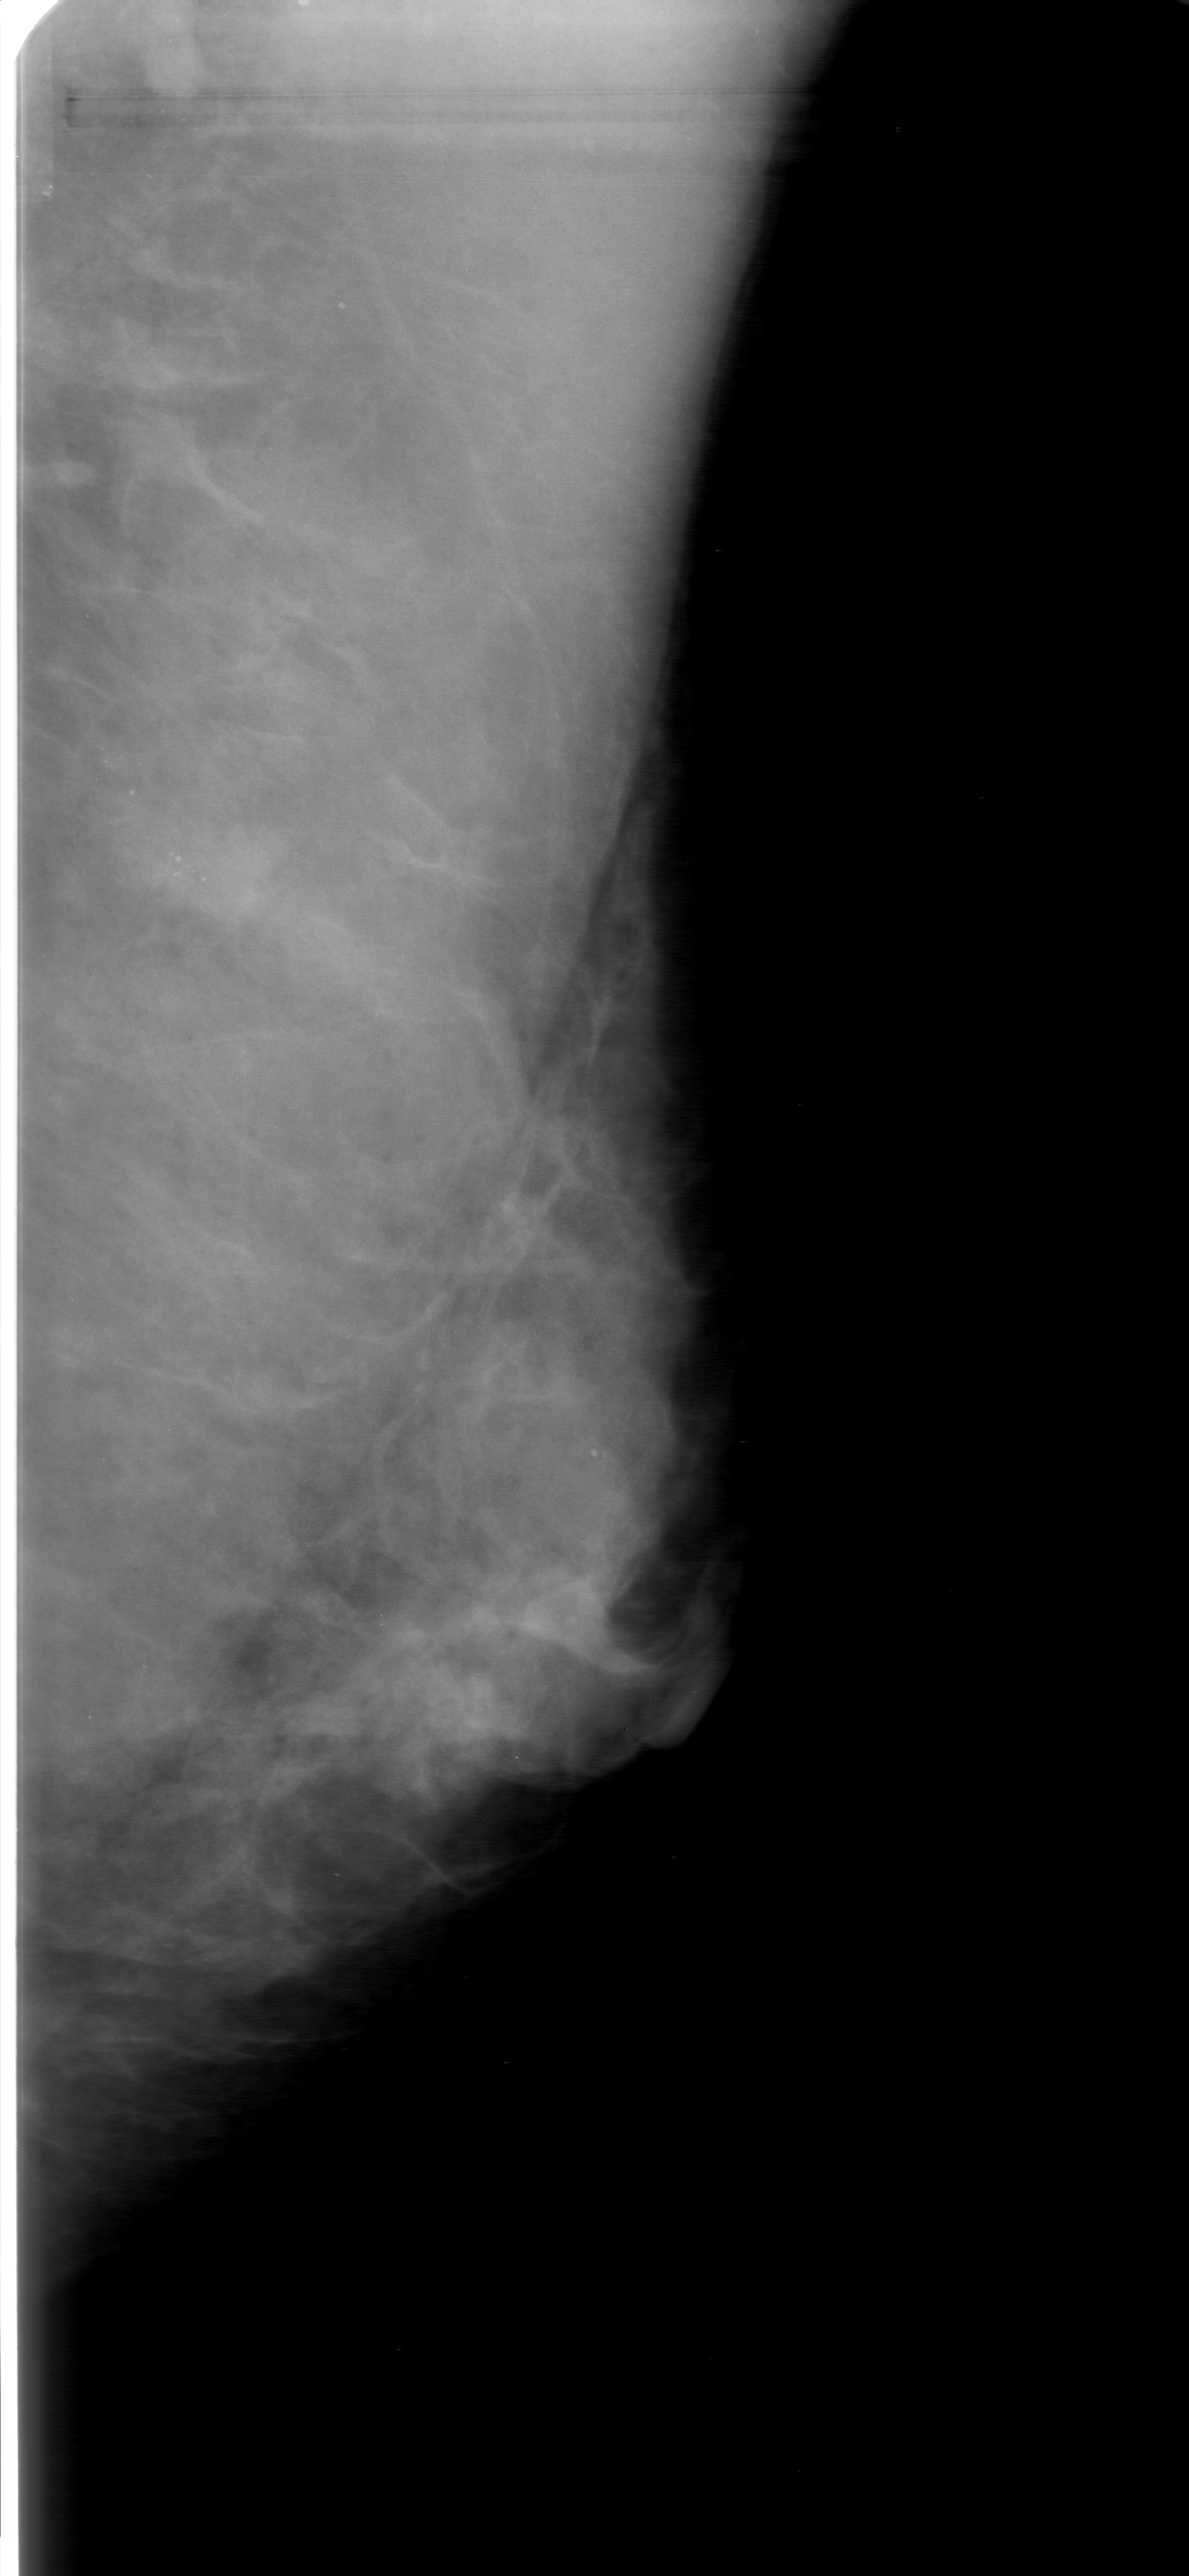
Scanned film-screen mammogram, left breast, MLO view, BI-RADS breast density category 3 (scale 1–4).
Calcifications, morphology round and regular / pleomorphic, distribution clustered; BI-RADS assessment category 0 (incomplete: needs additional imaging); subtlety rating 3 on a 1 (subtle) to 5 (obvious) scale; pathology (as recorded): benign.